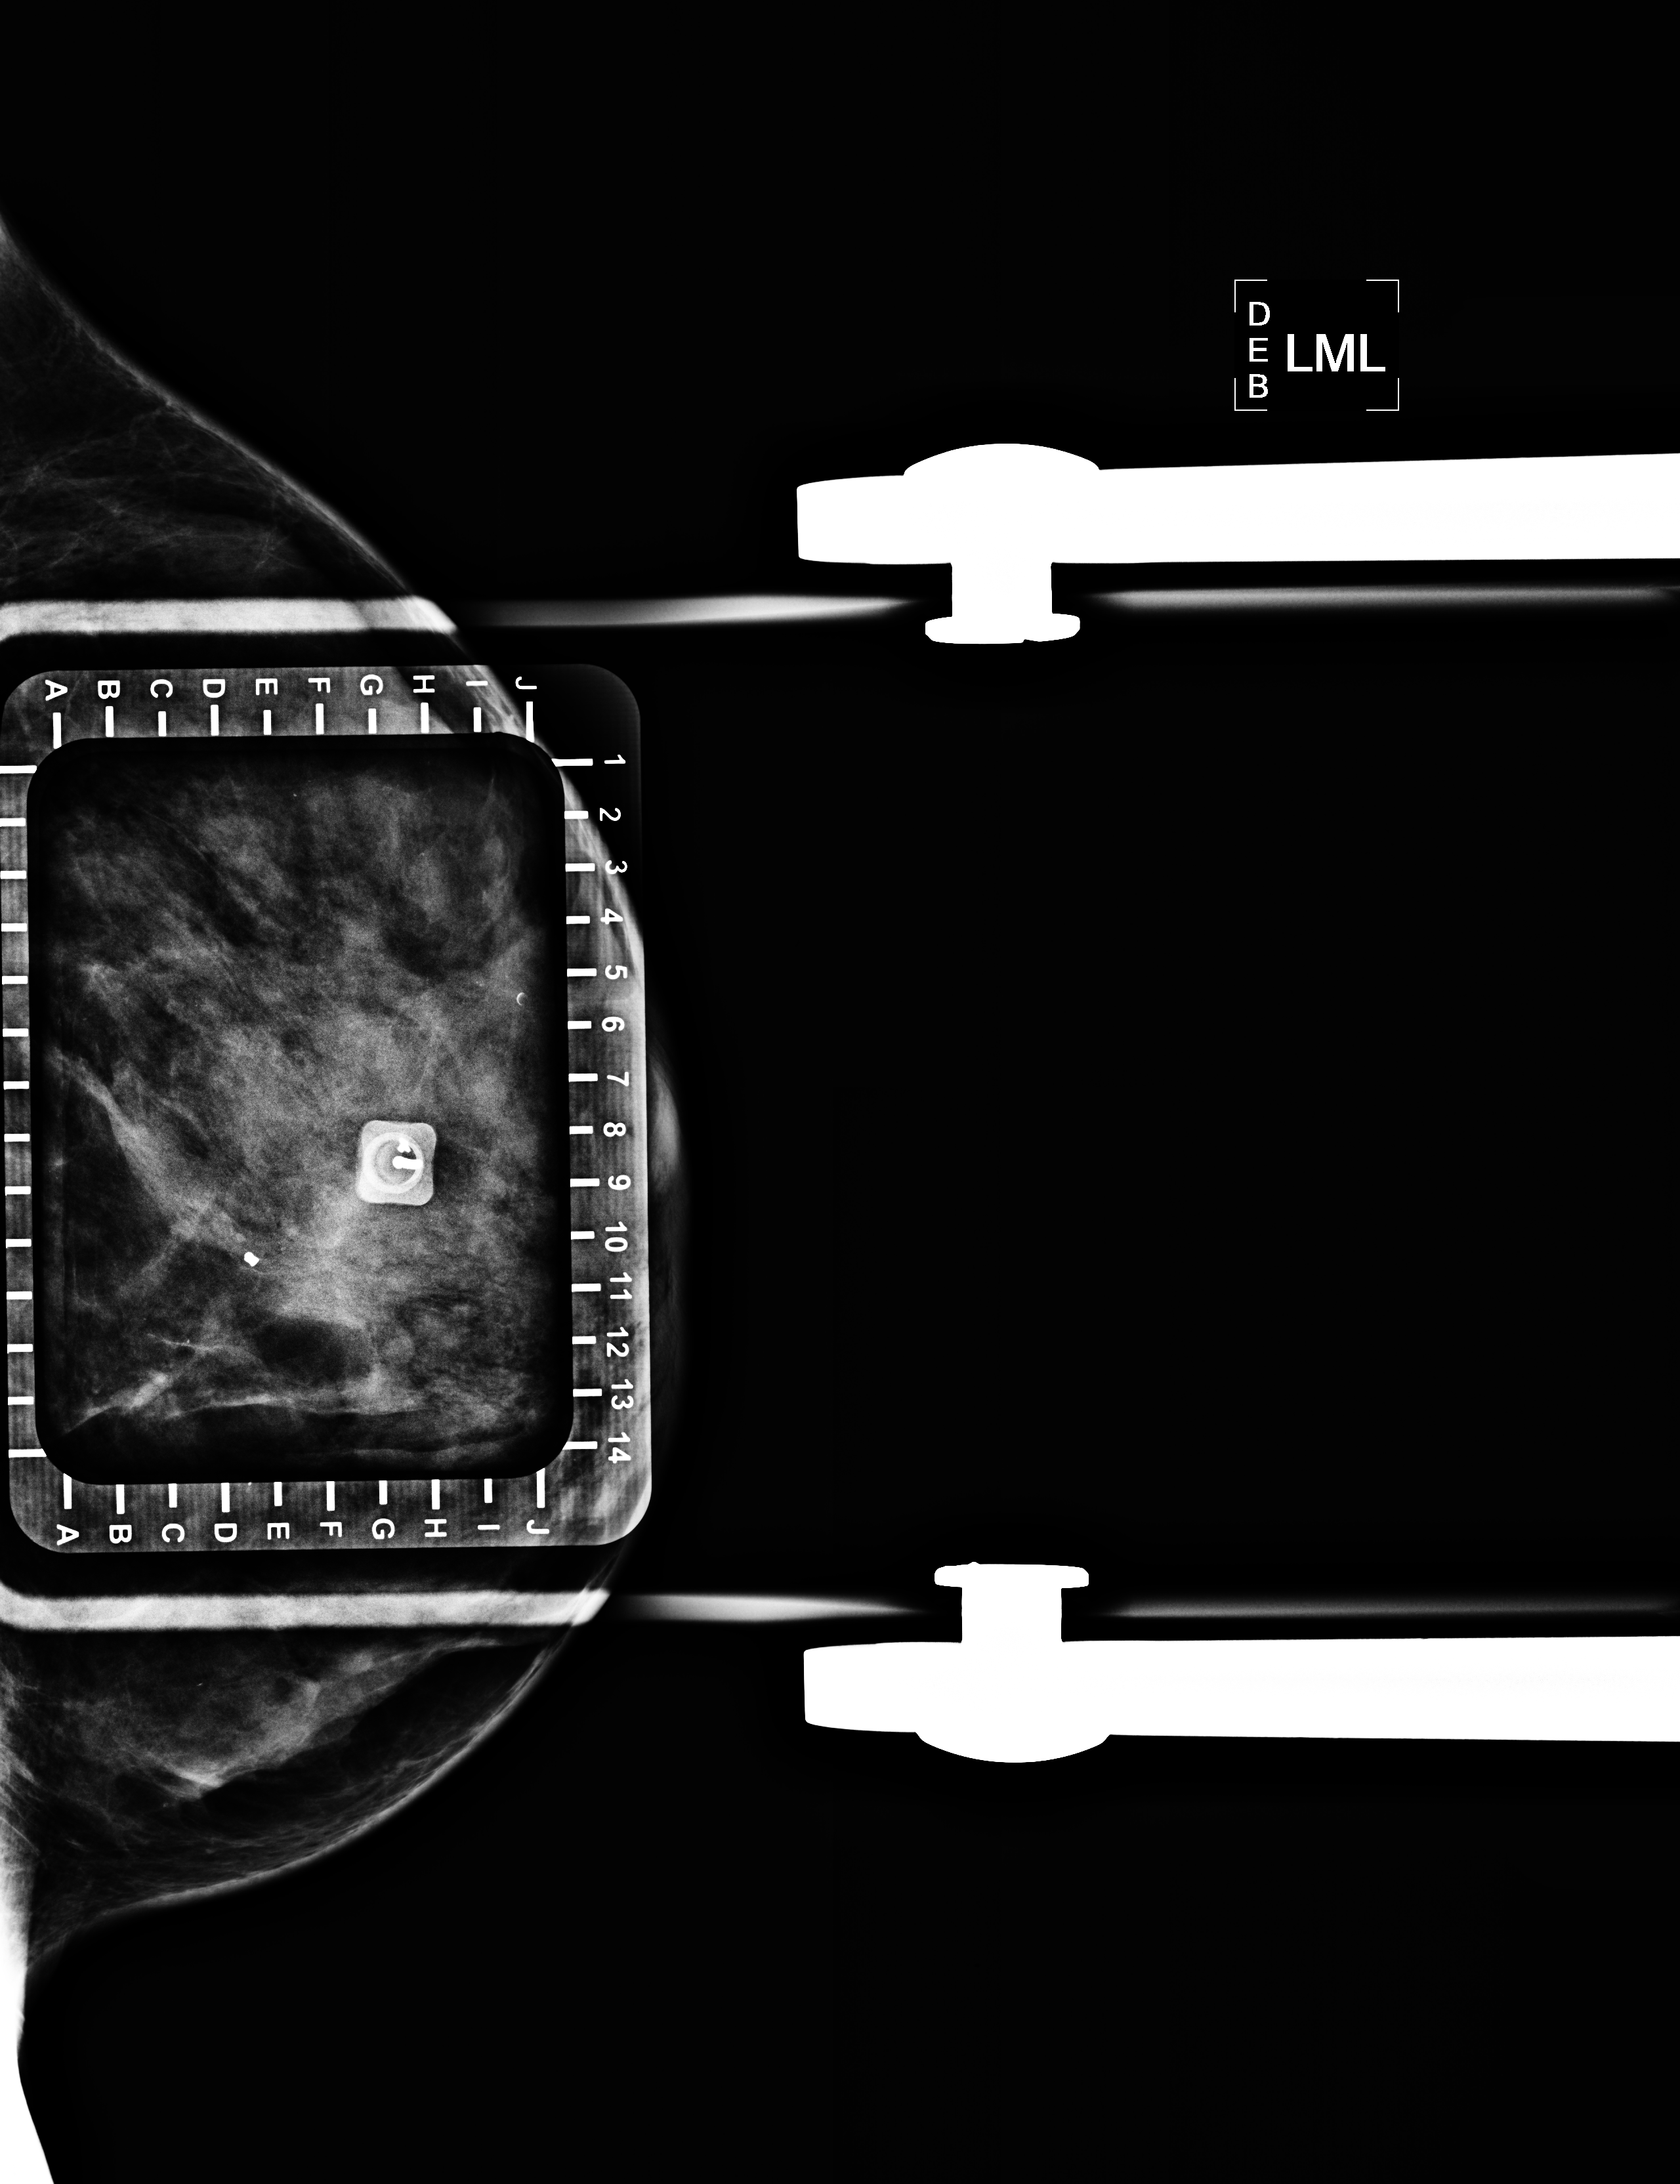
Needle-localisation mammographic view, left breast, ML view.
Pathology recorded for this patient (not read from this image): pathology diagnosis: ducta CA in situ (left breast); receptor status (as recorded): ER neg, PR neg, HER2 pos.